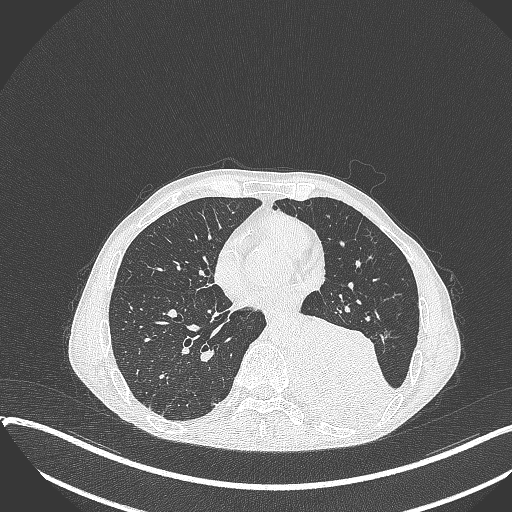
Chest CT, one axial slice. Slice 149 of 401 in the series (ordered by position). 120 kVp. Lung window (W 1500 / L -600 HU). 1 mm slice thickness. 512 × 512 image matrix, field of view 400 × 400 mm. Patient: male, 57 years. Case-level facts recorded for this patient, not image findings: clinical TNM (as recorded): T4 N0 M0.
Outlined on this slice (bounding box drawn by a radiologist):
- lung tumour (recorded histology: squamous cell carcinoma): bounding box [x1, y1, x2, y2] px = [298, 311, 406, 430]